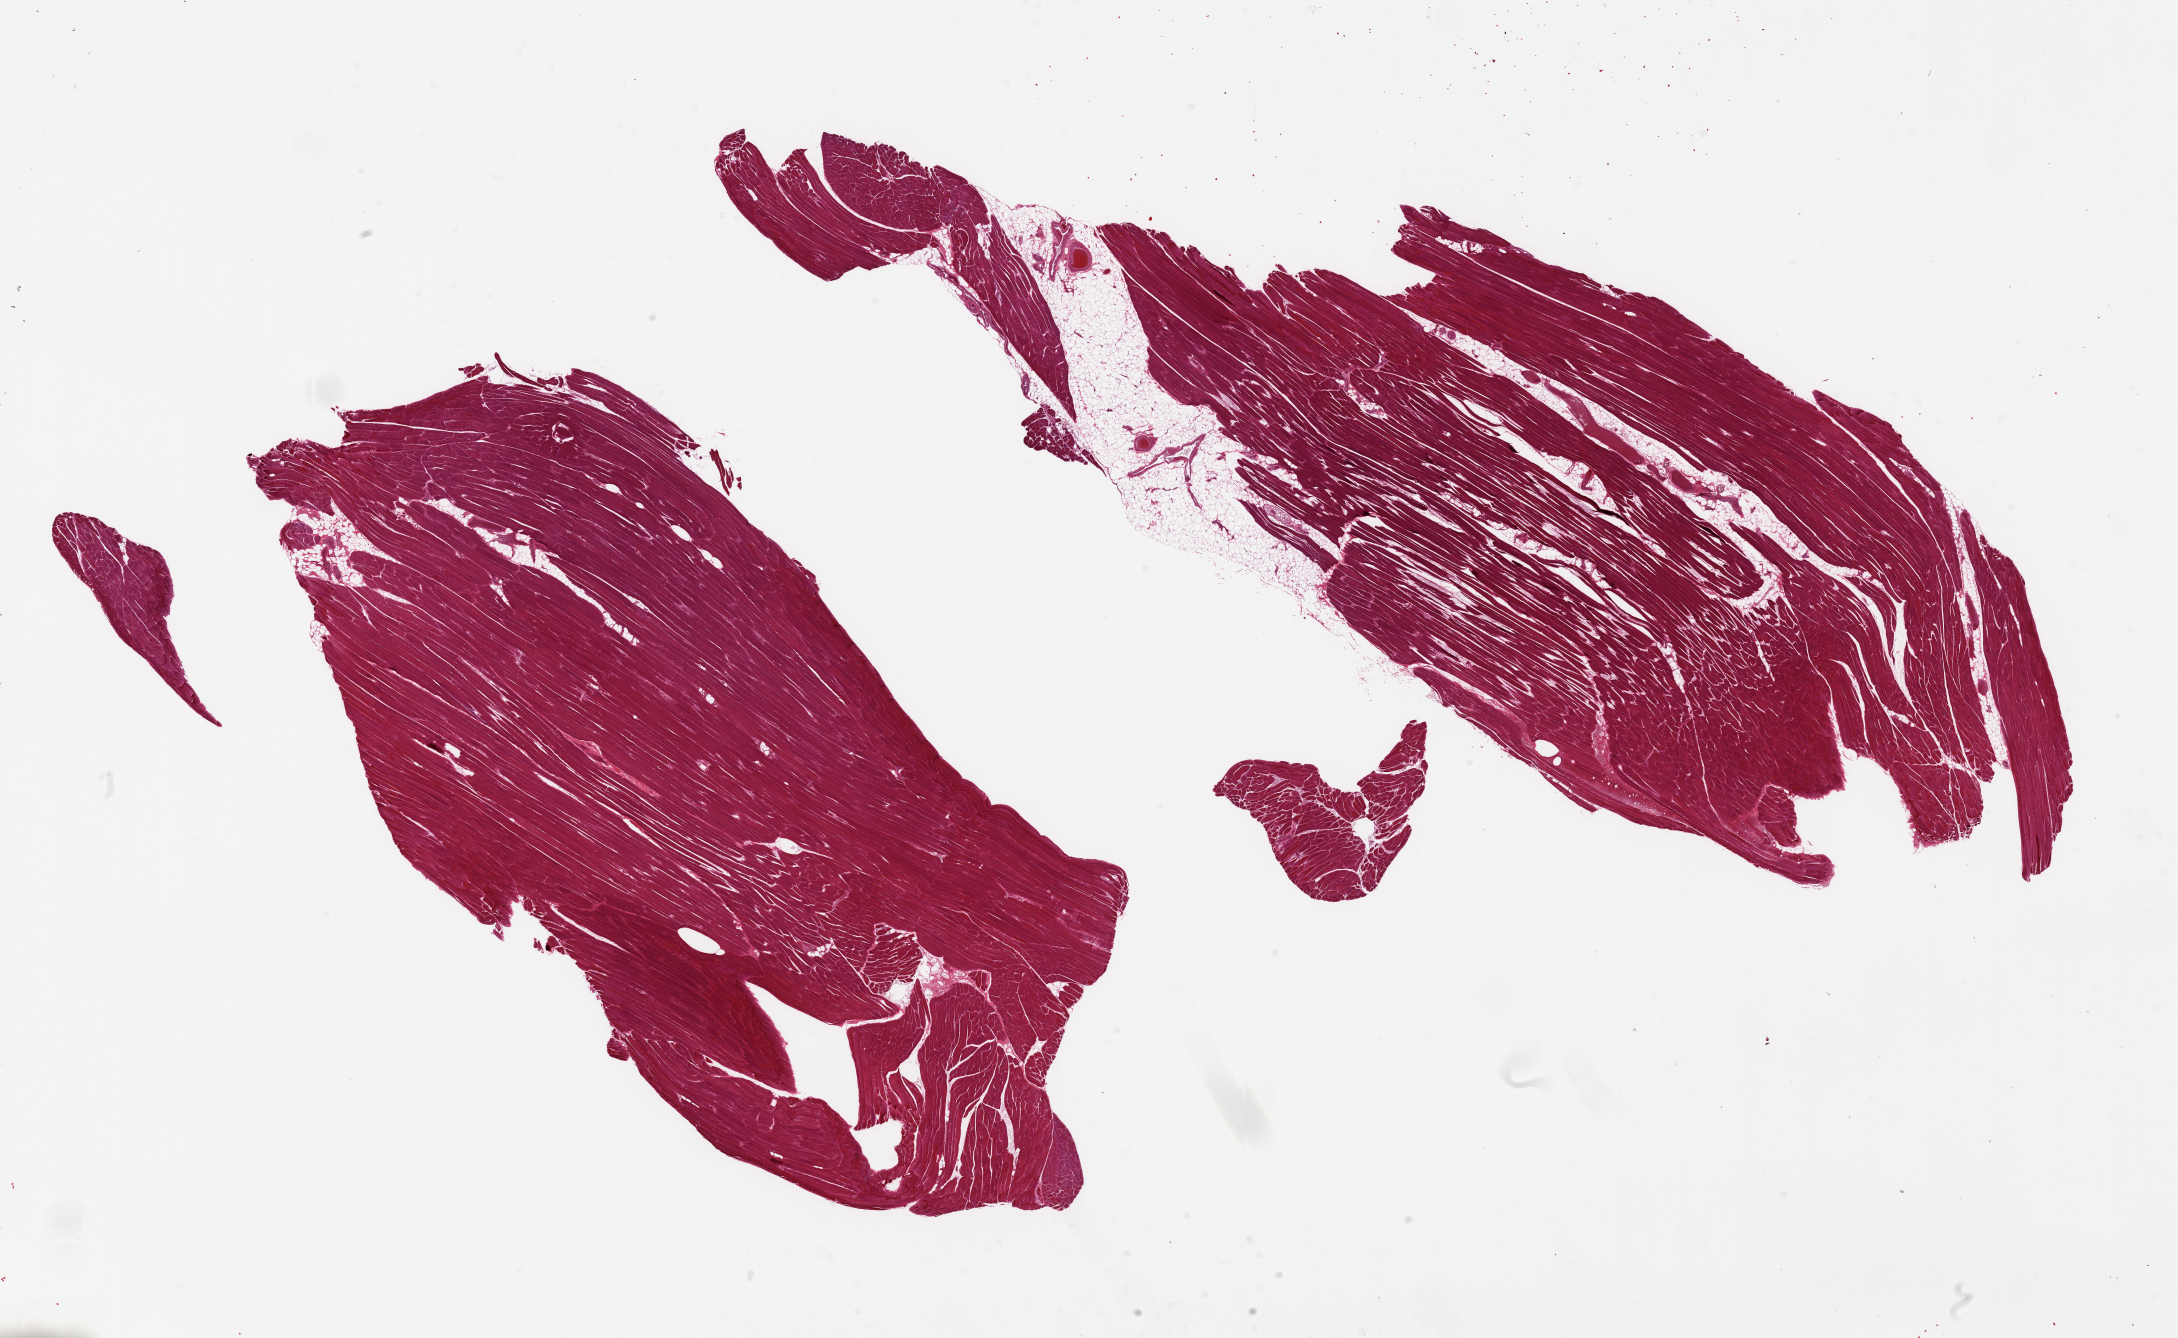
Digitized H&E-stained section, brightfield — shown as a low-resolution overview of the whole scanned area (about 34.5 x 21.2 mm). PAXgene-fixed paraffin-embedded (PFPE) section. Section of skeletal muscle (target tissue). Donor tissue sample. Male donor.
Review note (as recorded): 2 pieces, one piece includes ~10% internal fat.